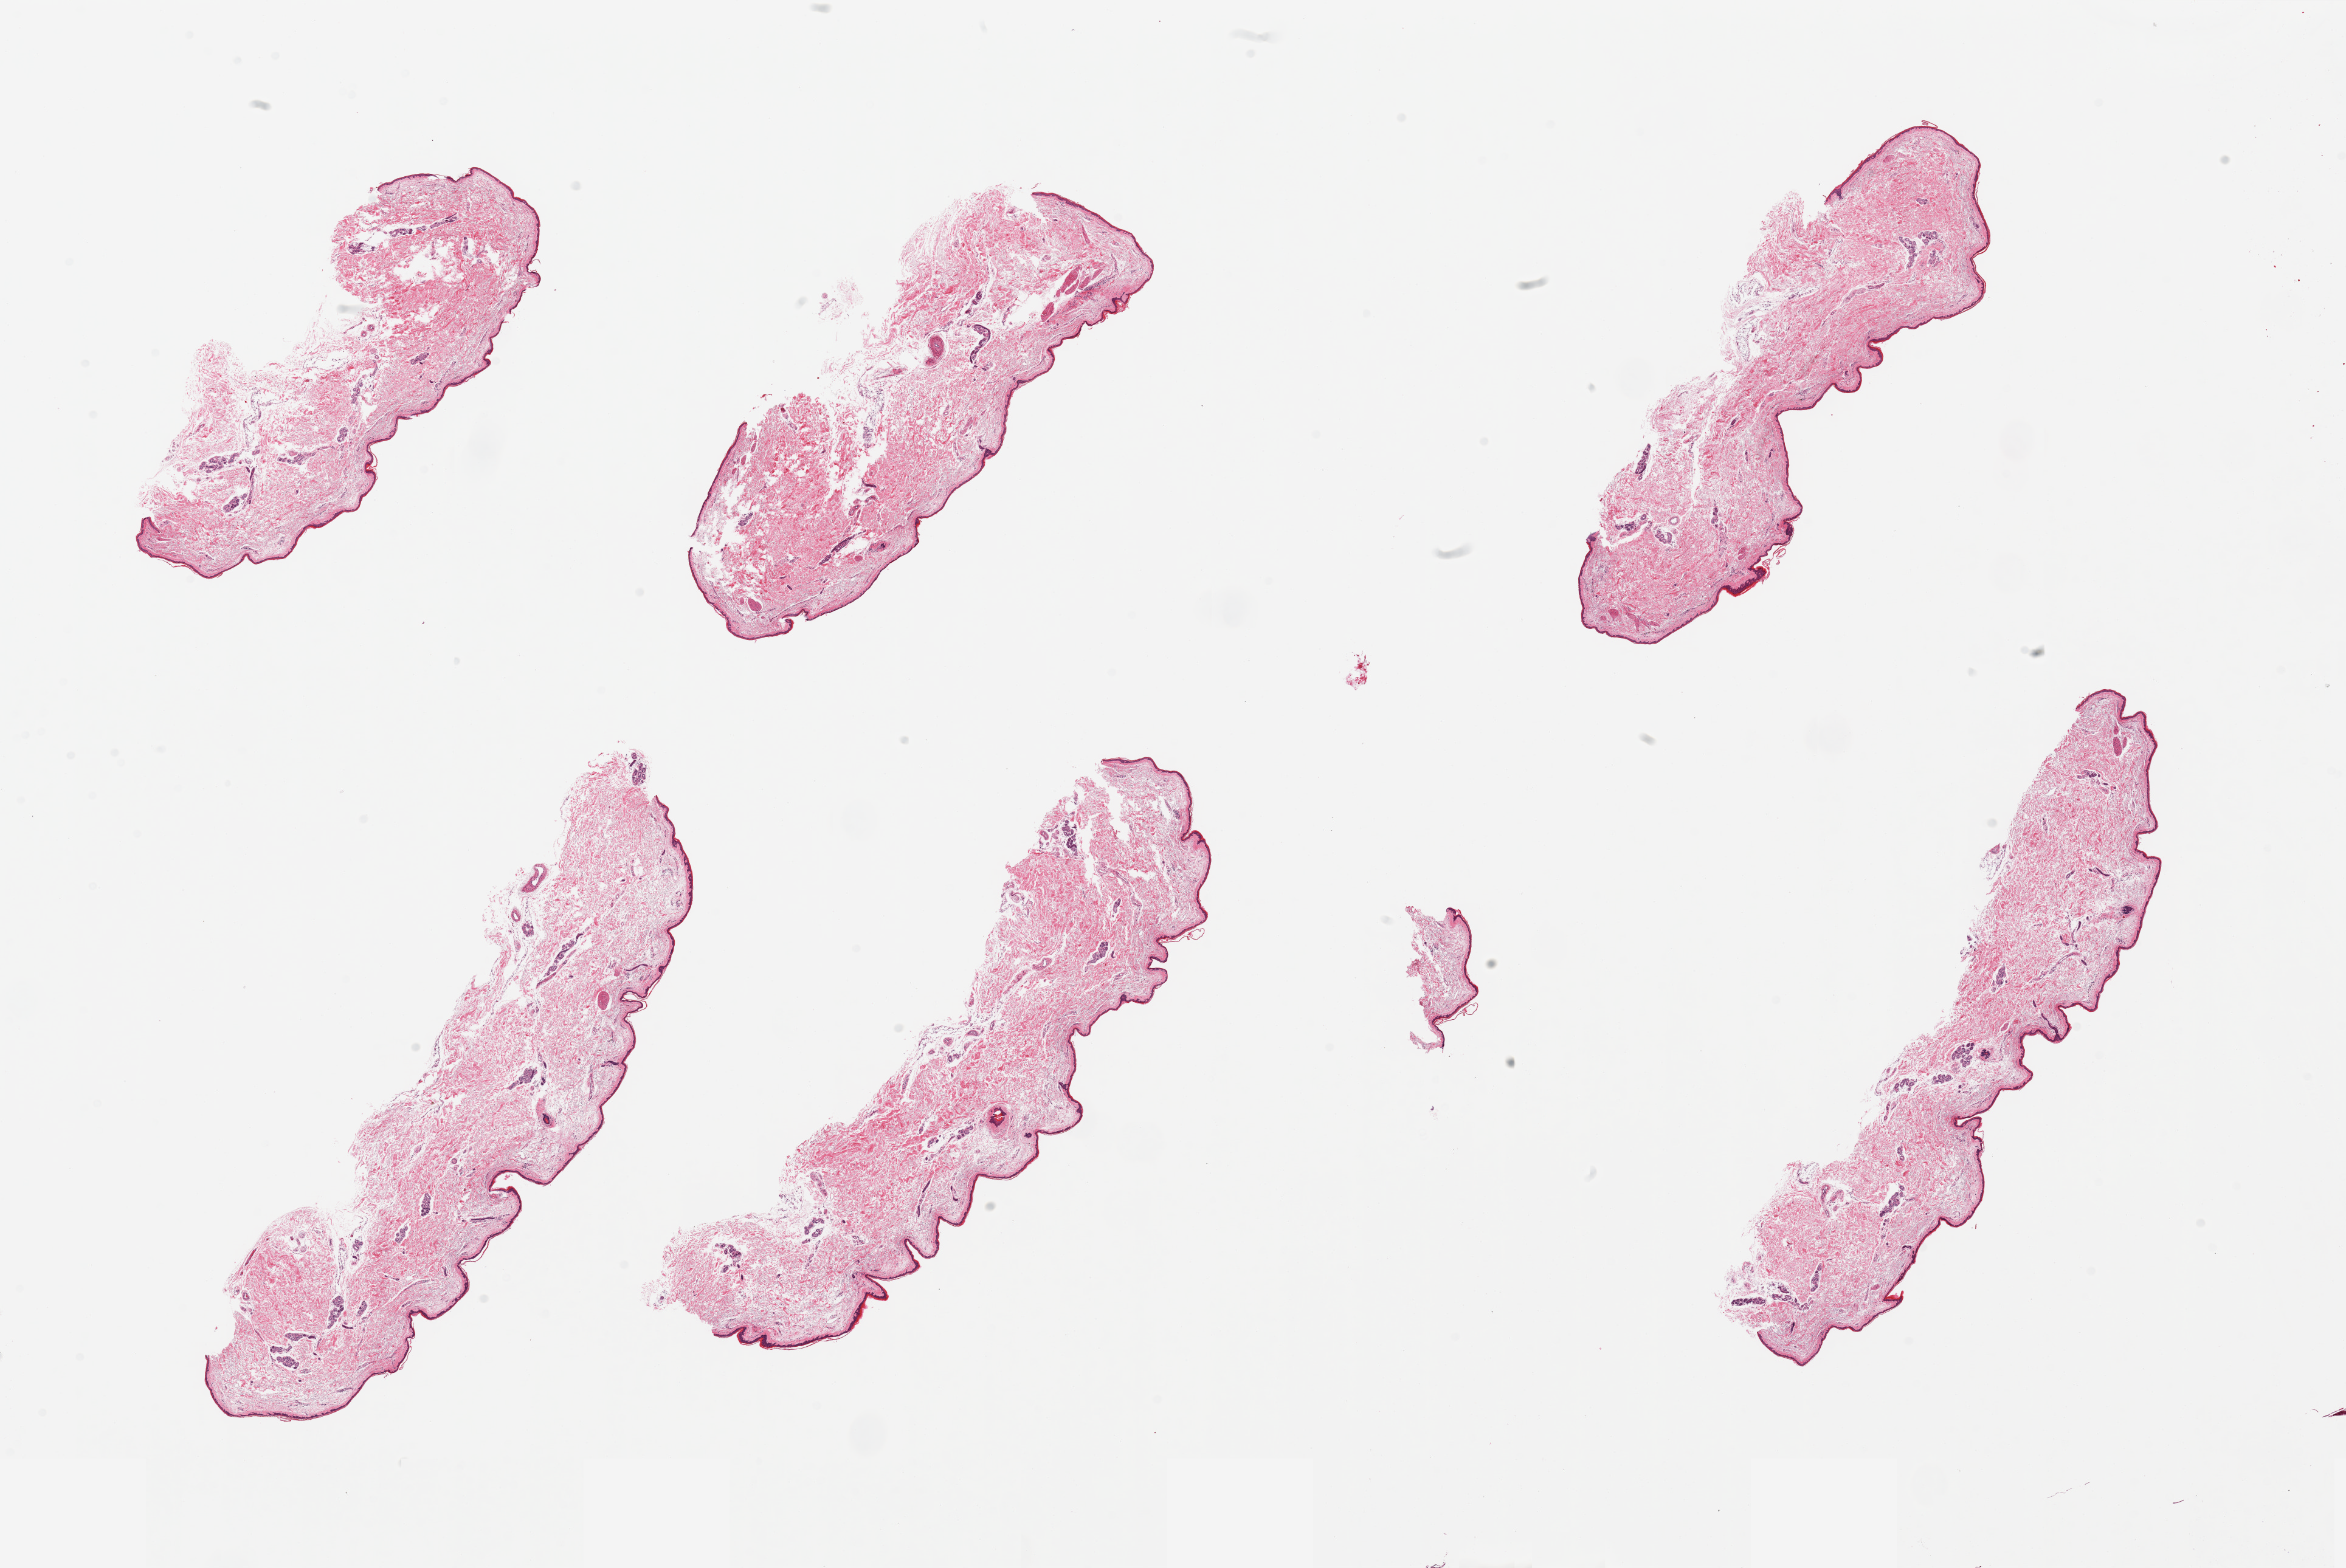
Haematoxylin and eosin whole-slide image — low-resolution overview of the scanned area, about 30.5 x 20.4 mm (from a 20x scan); PAXgene-fixed paraffin-embedded (PFPE) section; target tissue: skin of lower leg; donor tissue sample. Donor sex: male.
Reviewer comment on this tissue sample: 6 pieces, minimal dermal fat; squamous epithelium unusually atrophic, ~15-20 microns.